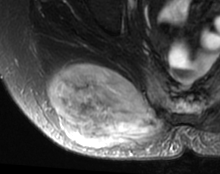
MRI of an extremity soft-tissue mass, one axial slice. T2-weighted fat-saturated. MR volume resampled by the dataset authors to the PET/CT grid (not the native acquisition matrix). 3.27 mm slice thickness. 220 × 174 image matrix. Female patient. From the clinical record (not read from this slice): histological type: spindle cell suggestive of myxofibrosarcoma; grade: intermediate; site of the primary tumour: right buttock.
Outlined on this slice (expert contour drawn on MRI and transferred to this co-registered scan by the dataset authors):
- gross tumour volume (mass): bounding box <49,63,167,147> (left, top, right, bottom; pixels)